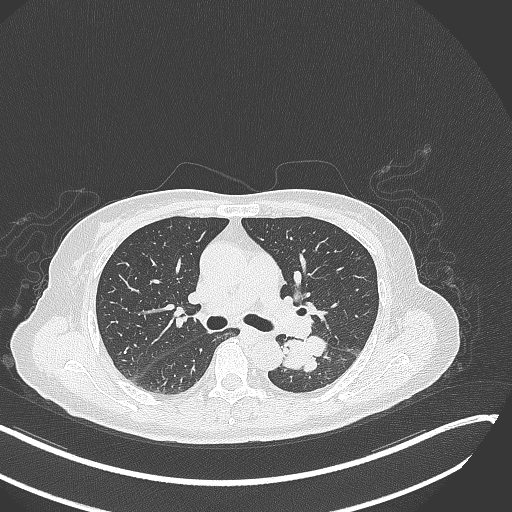
Chest CT, one axial slice; slice 172 of 342 in the series (ordered by position); 120 kVp; lung window (W 1500 / L -600 HU); 1 mm slice thickness; 512 × 512 image matrix, field of view 400 × 400 mm. Patient: female, 64 years. From the clinical record (not read from this slice): clinical TNM (as recorded): T3 N1 M1; histopathological grade: G3.
Annotated regions visible in this slice (bounding box drawn by a radiologist):
- lung tumour (recorded histology: small cell carcinoma): box from (x=282, y=332) to (x=329, y=378) px